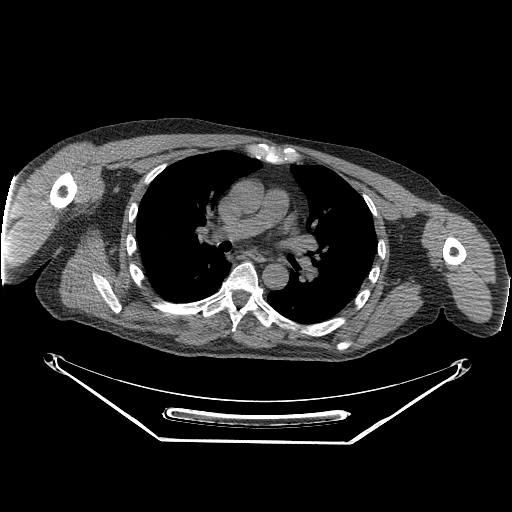
CT of an extremity soft-tissue mass (from a PET/CT study), one axial slice. Slice 177 of 267 in the series (ordered by position). Reconstruction kernel STANDARD. 140 kVp. Soft-tissue window (W 400 / L 40 HU). 3.75 mm slice thickness. 512 × 512 image matrix, field of view 500 × 500 mm. Male patient. Case-level facts recorded for this patient, not image findings: histological type: pleiomorphic spindle cell undifferentiated; grade: high; site of the primary tumour: right parascapusular.
Annotated regions visible in this slice (expert contour drawn on MRI and transferred to this co-registered scan by the dataset authors):
- gross tumour volume including surrounding oedema: bounding box <119,297,225,334> (left, top, right, bottom; pixels)